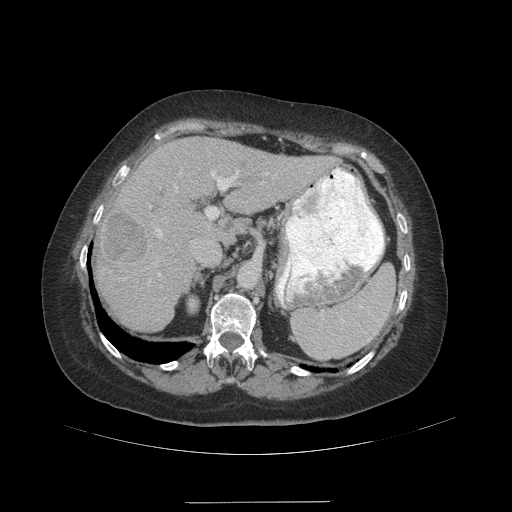
Contrast-enhanced abdominal CT (liver protocol), one axial slice; slice 68 of 99 in the series (ordered by position); reconstruction kernel STANDARD; 140 kVp; soft-tissue window (W 400 / L 40 HU); 2.5 mm slice thickness; 512 × 512 image matrix, field of view 440 × 440 mm. From the clinical record (not read from this slice): diagnosis: hepatocellular carcinoma (patient treated with transarterial chemoembolisation; whether this scan precedes or follows treatment is not stated here); TNM stage (as recorded): Stage-IVA; Child-Pugh class: A.
Annotated regions visible in this slice (semi-automatic segmentation, software-assisted and operator-edited):
- liver parenchyma outside the tumour (the mass and vessels are separate outlines, so this box may not span the whole liver): bounding box (x1, y1, x2, y2) in pixels: (94, 138, 330, 332)
- mass: (100, 212, 147, 263)
- liver vessels: (150, 169, 269, 277)